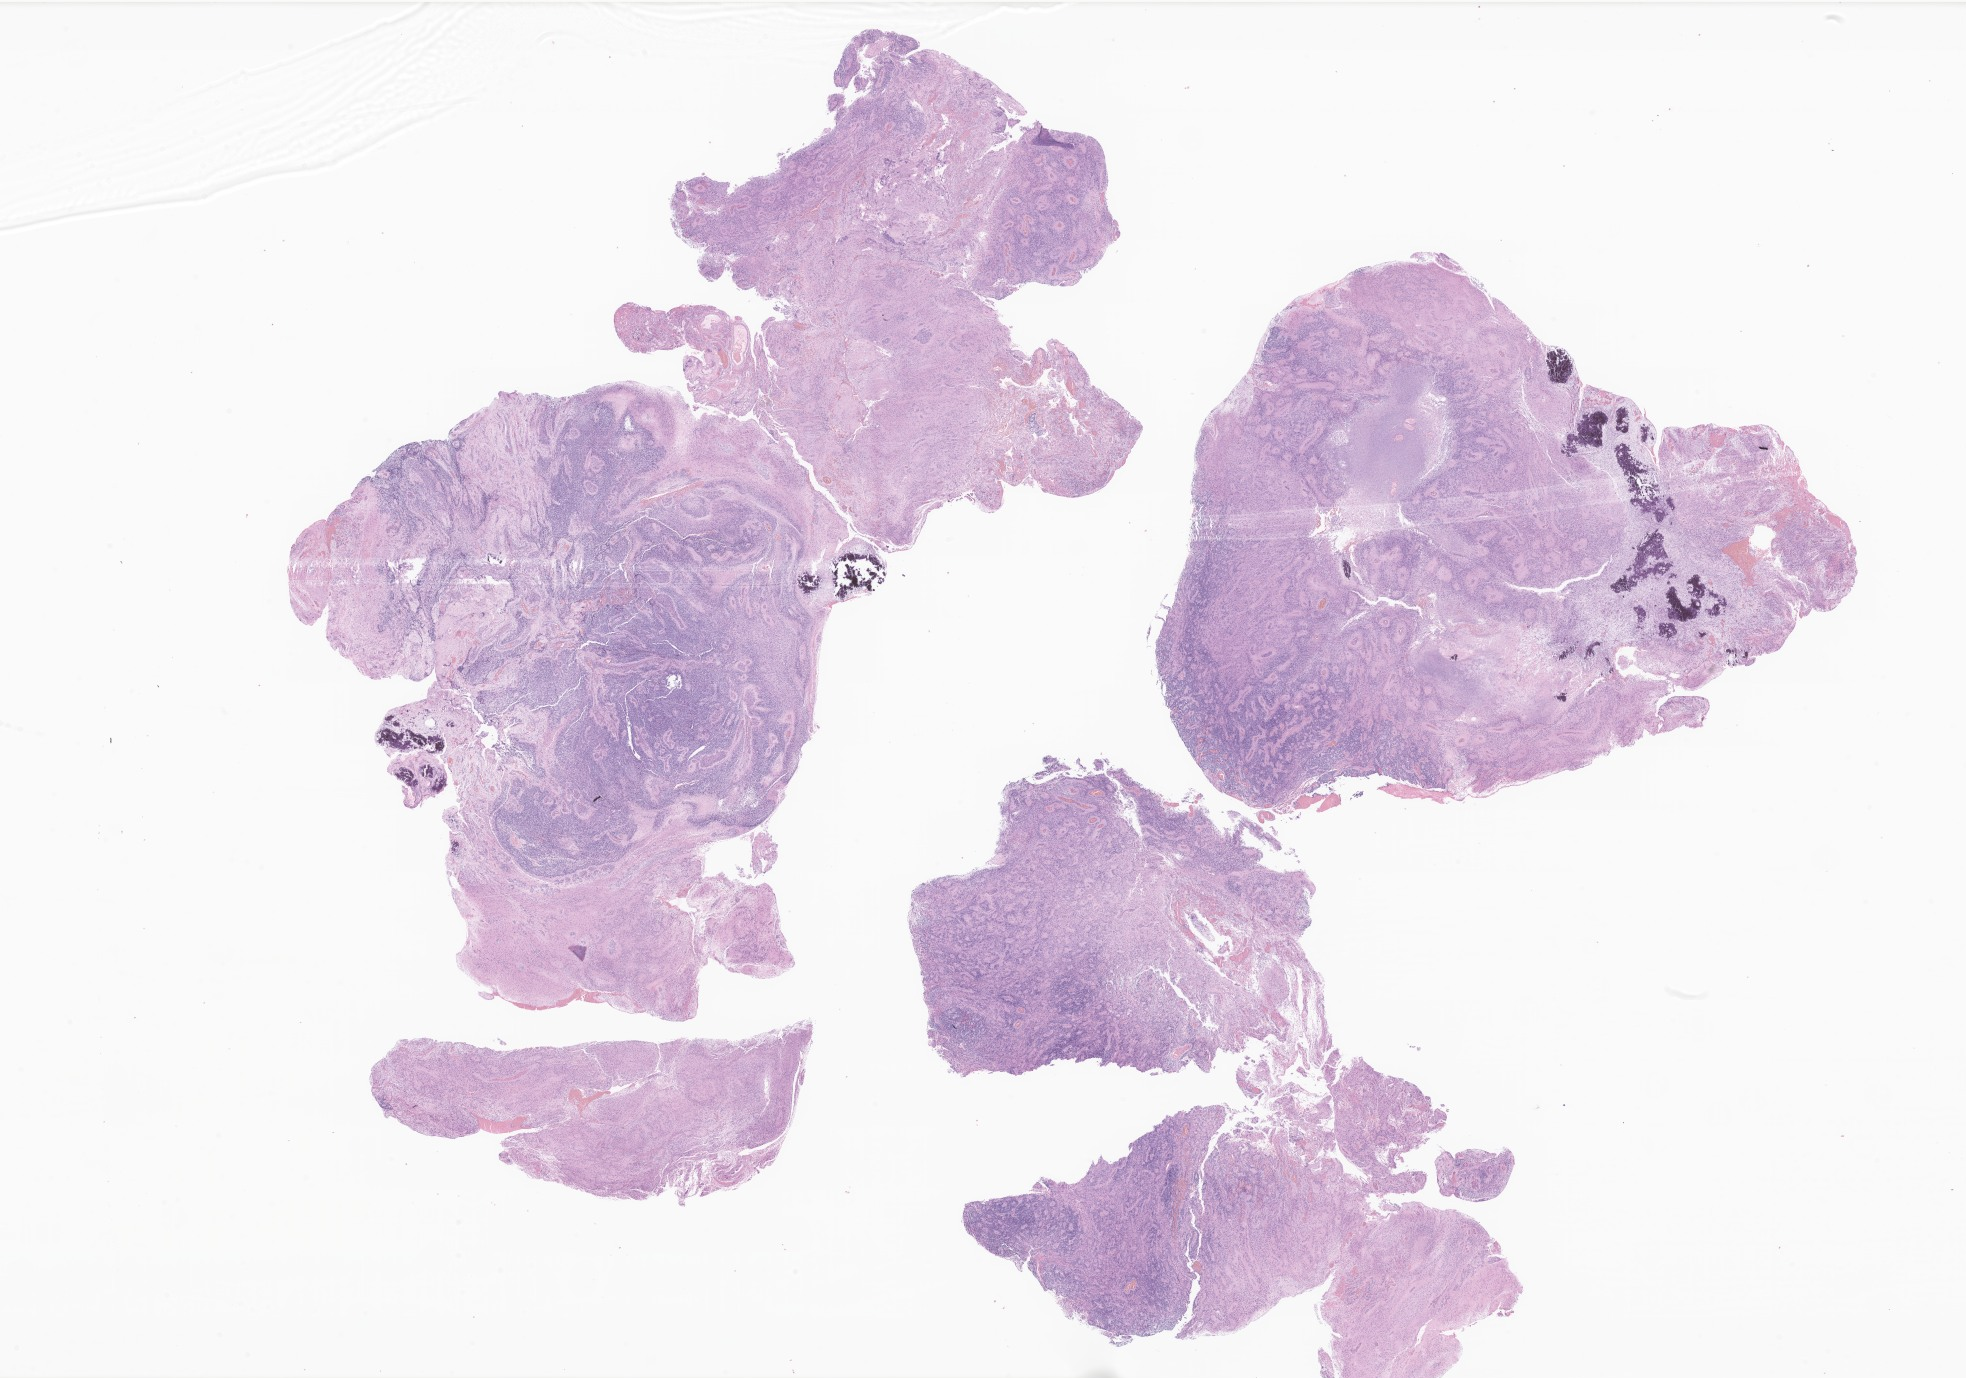
Digitized H&E-stained section of tumor tissue from the cerebellum — whole scanned area (about 33.2 x 23.2 mm) shown as a low-resolution overview, FFPE section. Male patient, age 535 days (about 1.5 years).
Recorded diagnosis: Ependymoma, NOS.